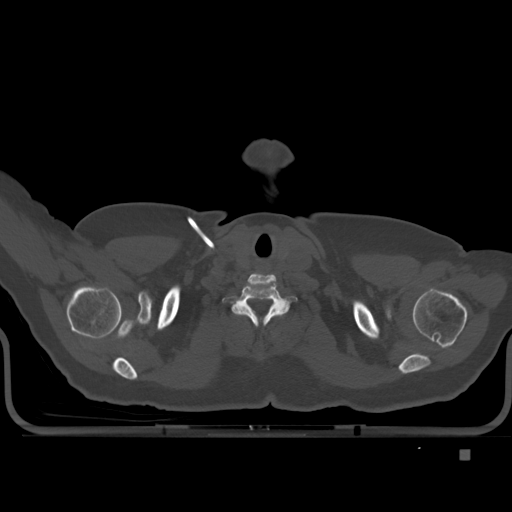
CT including the spine, one axial slice; position 410 of 477 along the scan axis; bone window (W 1800 / L 400 HU); 1.5 mm slice thickness; 512 × 512 image matrix, field of view 422 × 422 mm. Patient: female, 74 years. From the clinical record (not read from this slice): primary cancer: colon.
Outlined on this slice (semi-automatically segmented with operator editing):
- T1 vertebra: box from (x=252, y=307) to (x=285, y=324) px